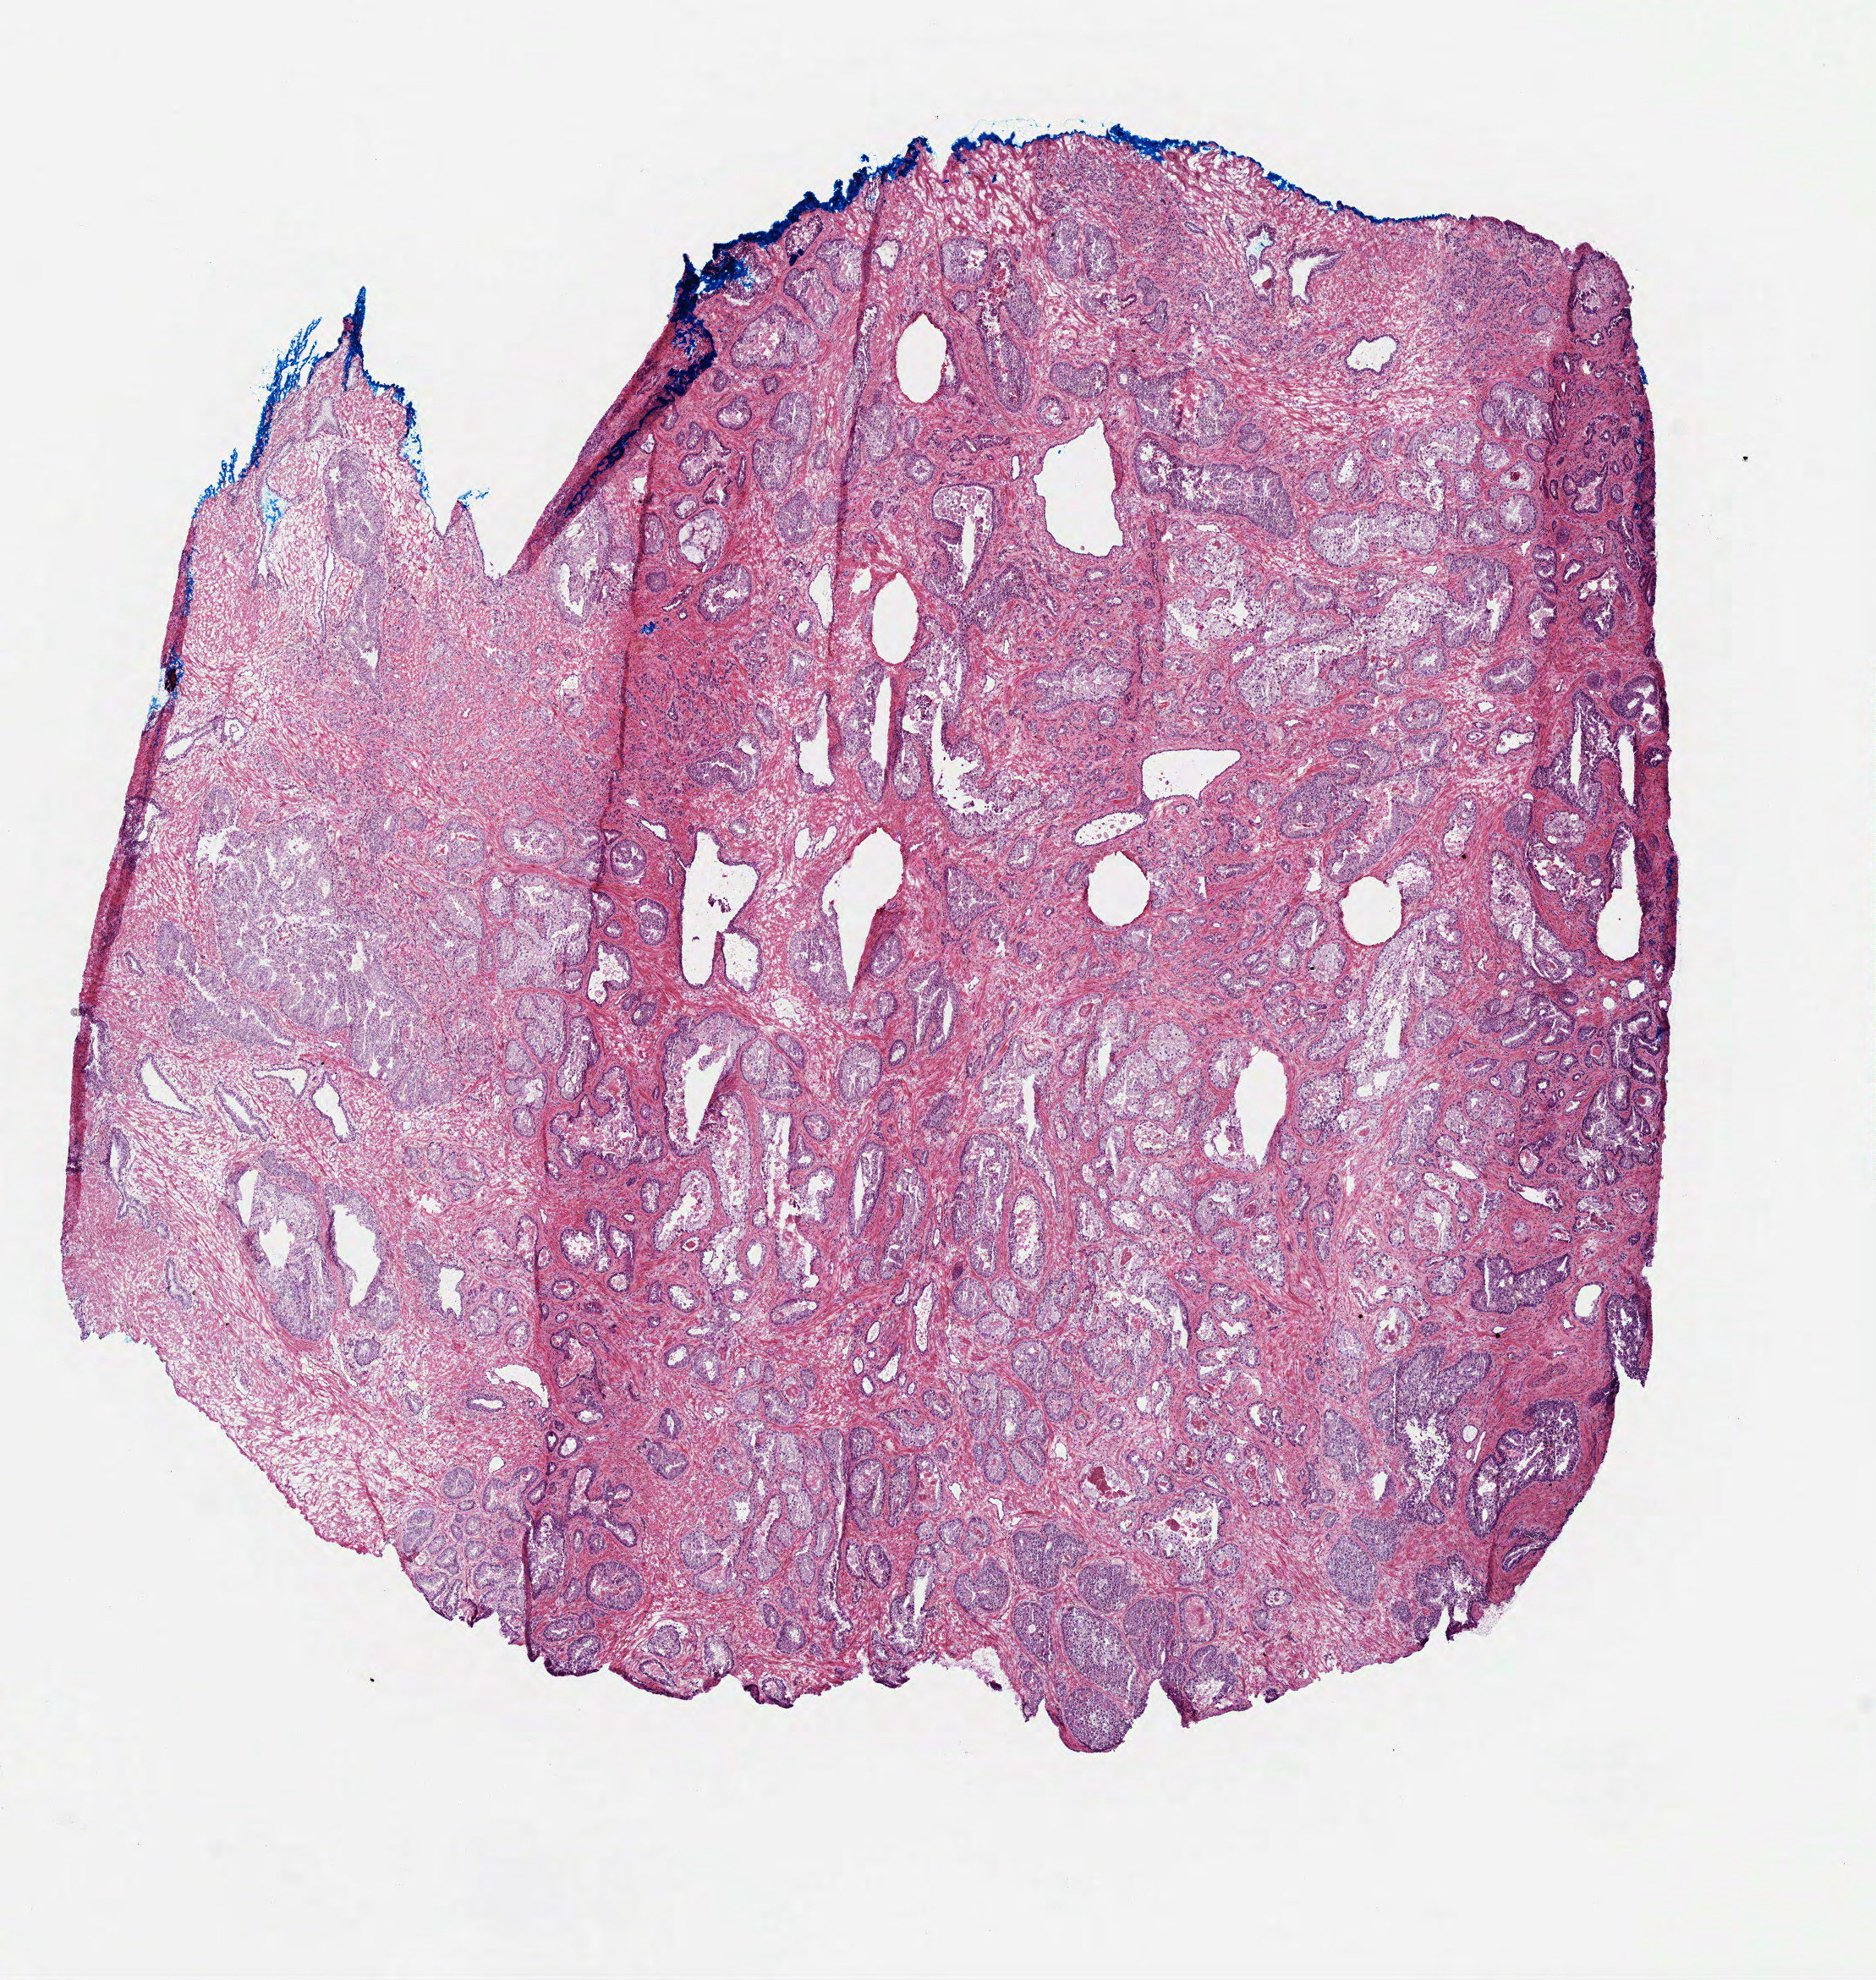
H&E whole-slide image, whole scanned area (about 8.9 x 9.4 mm, acquisition: 40x scan) shown as a low-resolution overview, formalin-fixed paraffin-embedded (FFPE) diagnostic section, primary tumour sample from the colon. Male, age 80 years at initial diagnosis.
AJCC pathologic stage: IIA (7th edition). Histologic diagnosis: Mucinous adenocarcinoma (hepatic flexure of colon). Lymph nodes positive (case pathology): 0 of 18 examined.